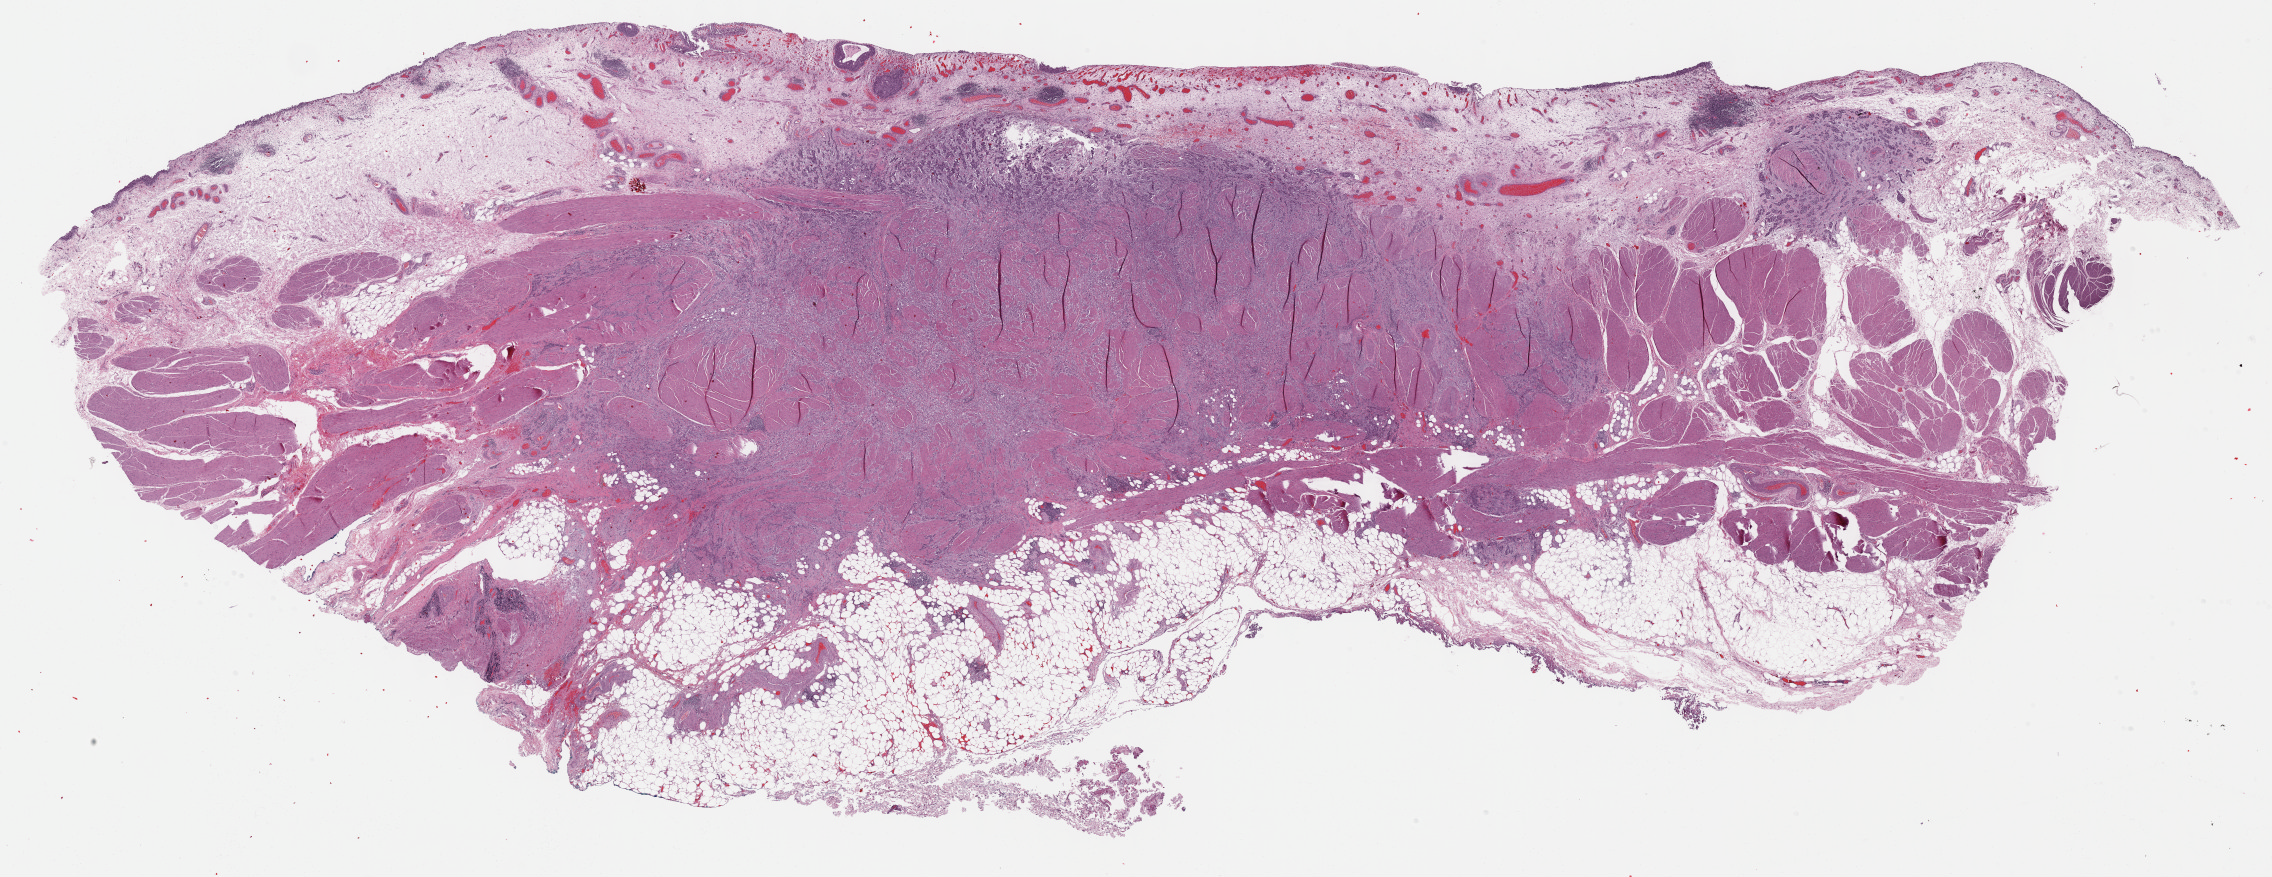
H&E-stained whole-slide image — shown as a low-resolution overview of the whole scanned area (about 36.7 x 14.2 mm); FFPE section; bladder, primary tumour sample. Patient: male, age at initial diagnosis 74 years. Histologic grade: high grade.
TNM: T3 N0 M0. Histologic diagnosis: Transitional cell carcinoma. AJCC pathologic stage: III (6th edition).